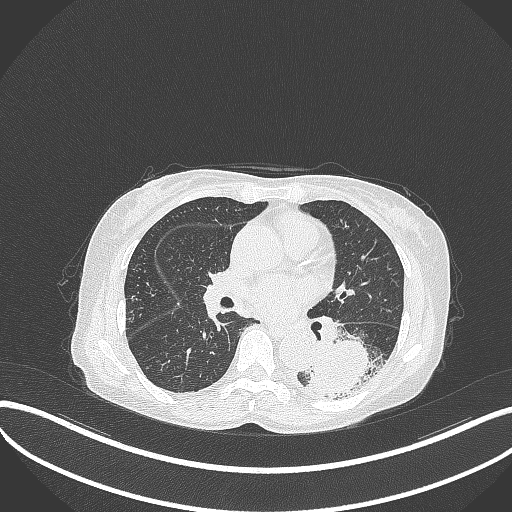
Chest CT, one axial slice. Position 160 of 370 along the scan axis. Reconstruction kernel B70f. 120 kVp. Lung window (W 1500 / L -600 HU). 1 mm slice thickness. 512 × 512 image matrix. Patient: female, 78 years. From the clinical record (not read from this slice): clinical TNM (as recorded): T3 N0 M1.
Outlined on this slice (bounding box drawn by a radiologist):
- lung tumour (recorded histology: squamous cell carcinoma): bounding box <305,336,389,400> (left, top, right, bottom; pixels)